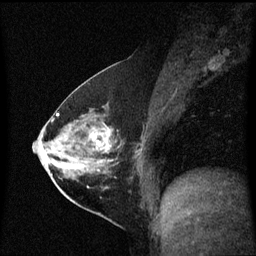
Breast MRI (dynamic contrast-enhanced), one sagittal slice; dynamic contrast-enhanced series, image 2 of 3 at this slice position (ordered by acquisition); 1.5 T; TE 4.2 ms, TR 8.4 ms; 2 mm slice thickness; 256 × 256 image matrix, field of view 210 × 210 mm. Female patient, age 54 years. From the clinical record (not read from this slice): setting: breast cancer imaged before/during neoadjuvant chemotherapy; receptor status: HER2-positive.
Annotated regions visible in this slice (semi-automatic segmentation, software-assisted and operator-edited):
- analysis volume of interest (the breast-tissue region the enhancement analysis was run in; not a lesion): bounding box <59,115,141,199> (left, top, right, bottom; pixels)
- tumour enhancement mask (voxels above the 70 % enhancement threshold inside the analysis volume of interest): <63,128,112,172>